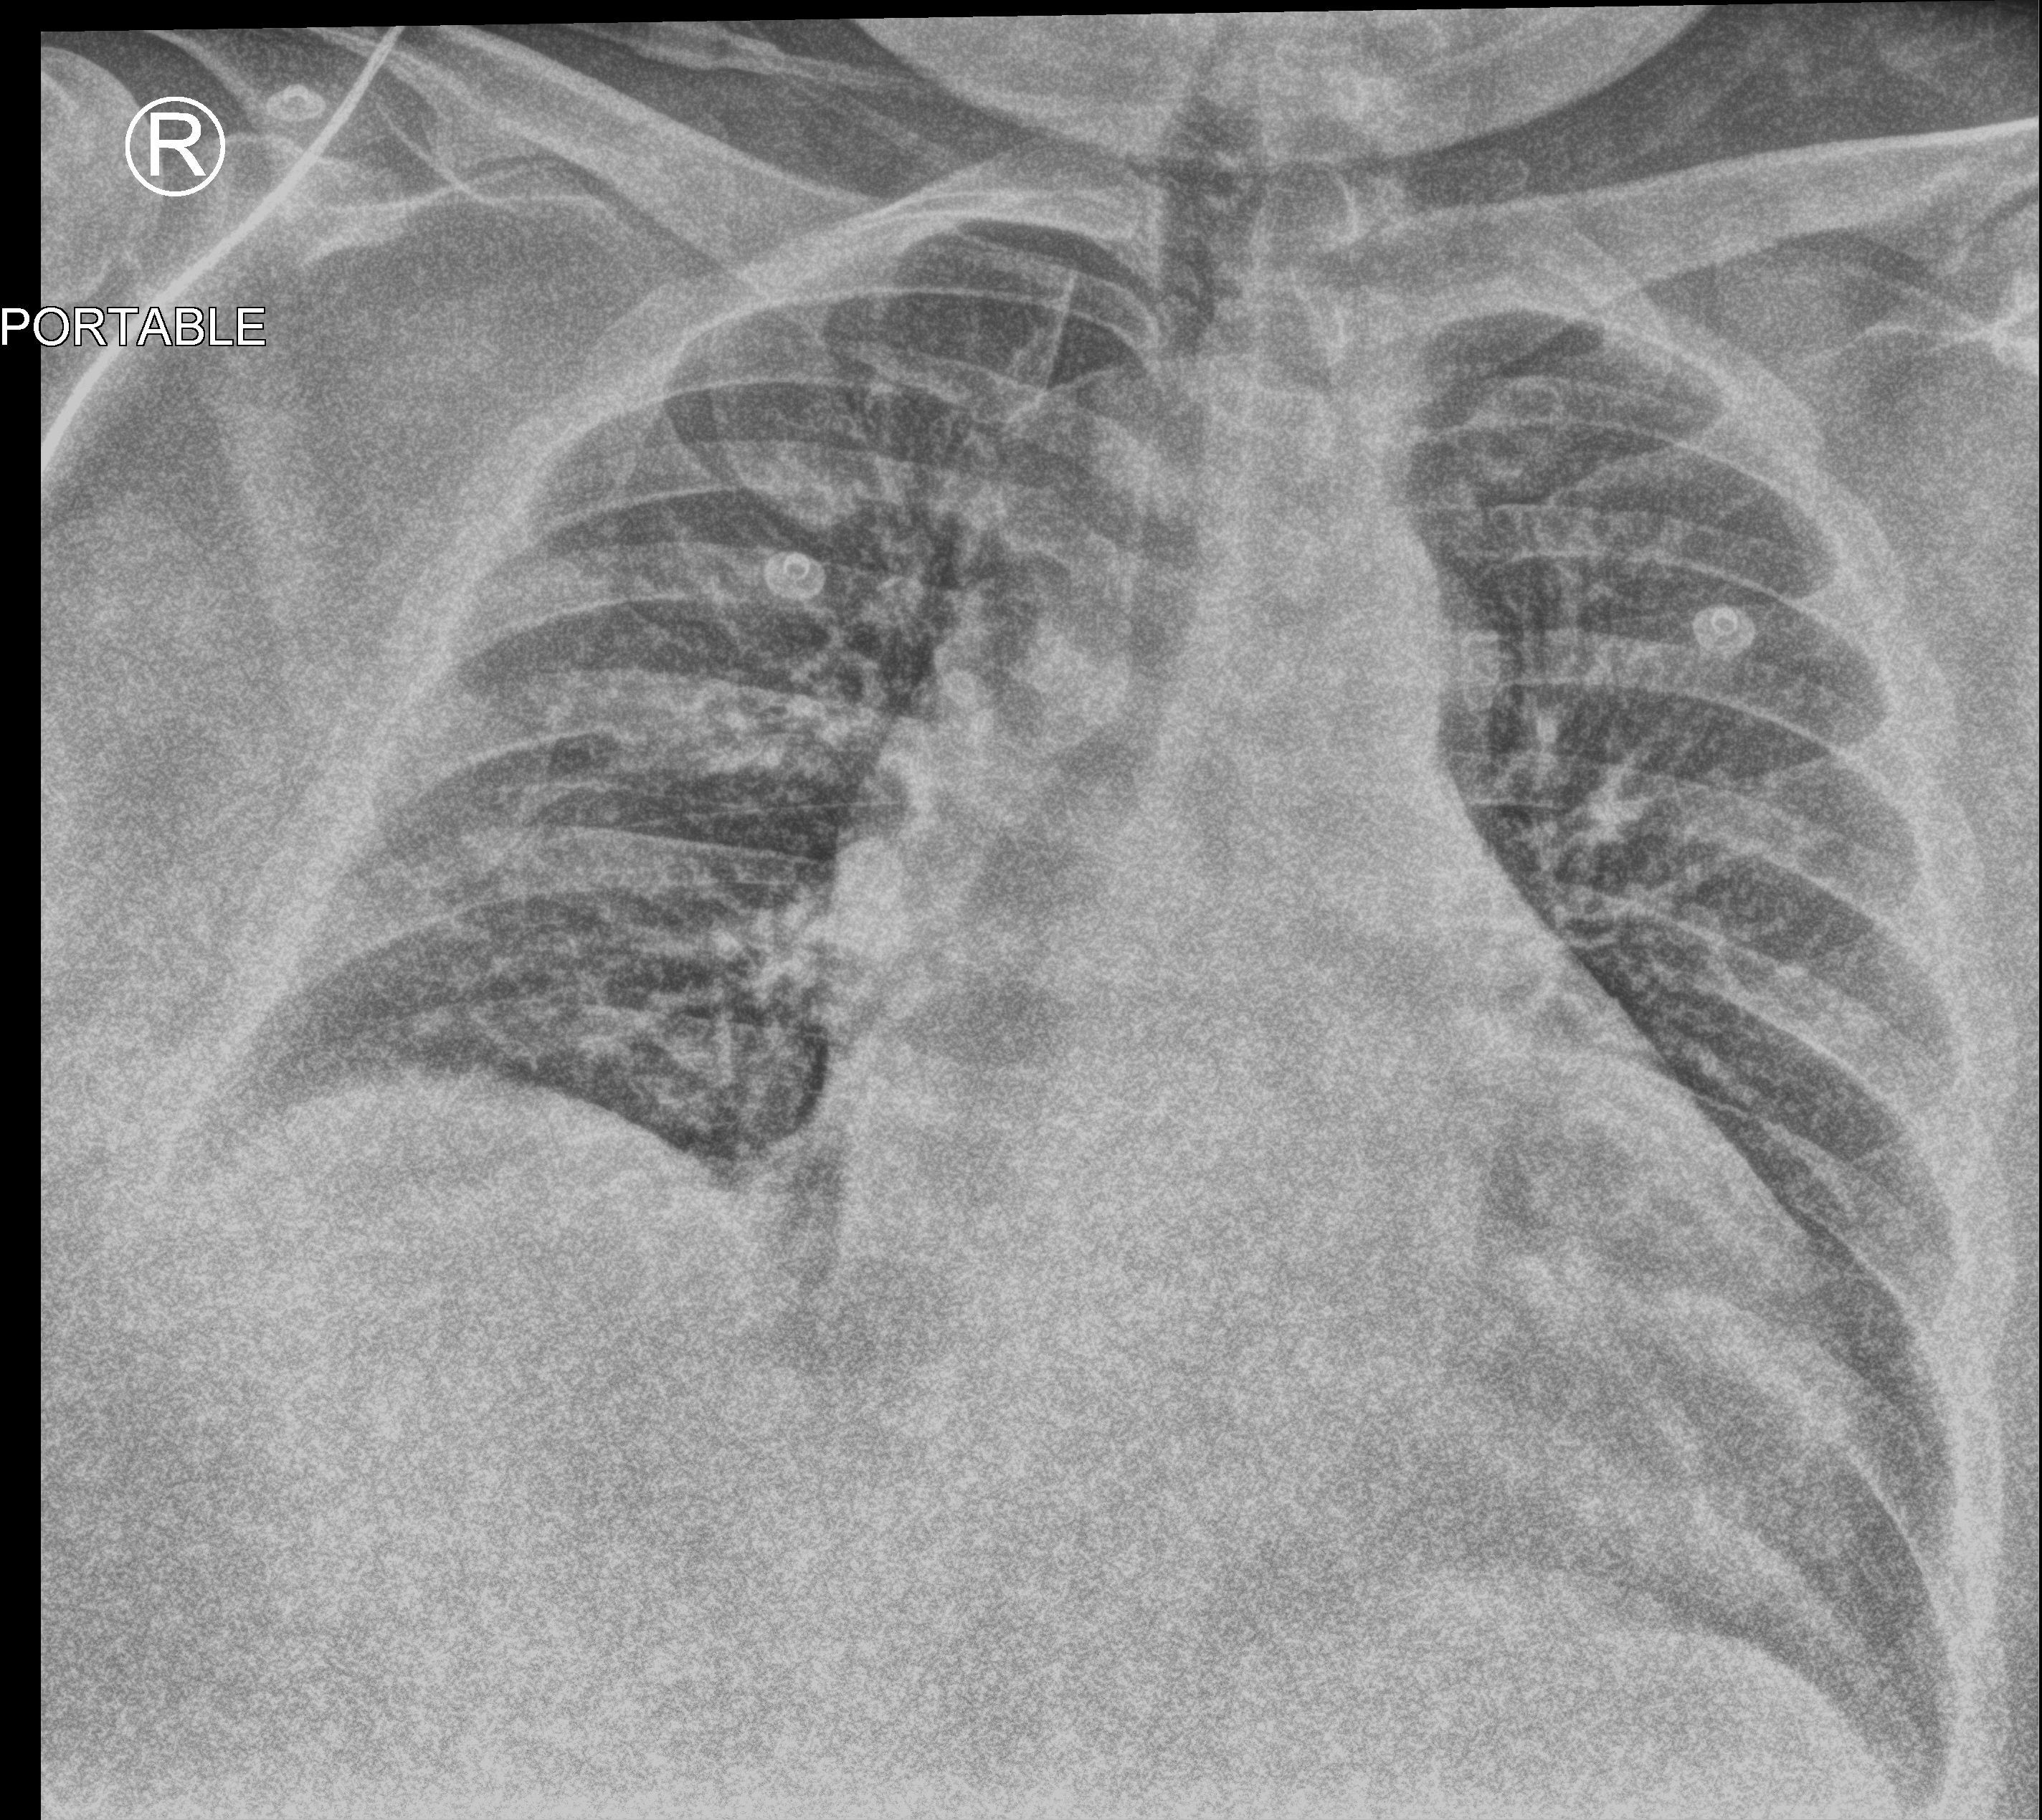
Portable chest radiograph; anteroposterior (AP) projection. Male patient hospitalised with COVID-19, age 18–59 years.
From the hospital-stay record, not from the radiograph (when in the stay this image was taken is not recorded): admitted to intensive care during this hospital stay: no; chronic kidney disease (admission record): no; mechanically ventilated during this hospital stay: no.